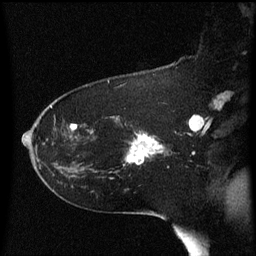
Breast MRI (dynamic contrast-enhanced), one sagittal slice; position 40 of 60 along the scan axis; dynamic contrast-enhanced series, image 2 of 3 at this slice position (ordered by acquisition); 1.5 T; TE 4.2 ms, TR 8.4 ms; 2 mm slice thickness; 256 × 256 image matrix. Patient: female, 54 years. From the clinical record (not read from this slice): setting: breast cancer imaged before/during neoadjuvant chemotherapy; receptor status: HR-positive, HER2-negative.
Outlined on this slice (semi-automatically segmented with operator editing):
- analysis volume of interest (the breast-tissue region the enhancement analysis was run in; not a lesion): bounding box <128,134,164,165> (left, top, right, bottom; pixels)
- tumour enhancement mask (voxels above the 70 % enhancement threshold inside the analysis volume of interest): <128,134,163,165>